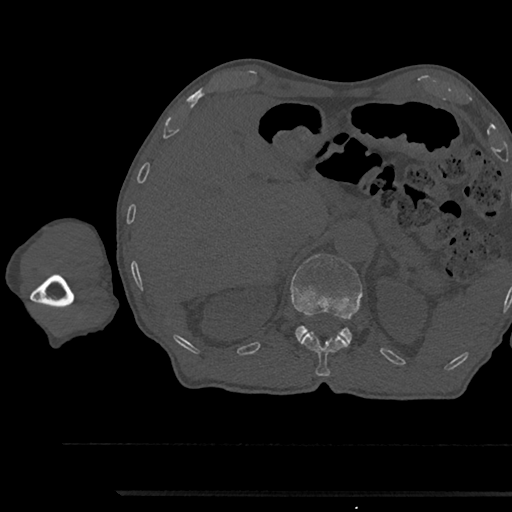
CT including the spine, one axial slice; slice 679 of 797 in the series (ordered by position); bone window (W 1800 / L 400 HU); 0.5 mm slice thickness; 512 × 512 image matrix, field of view 367 × 367 mm. Male patient, age 79 years. From the clinical record (not read from this slice): primary cancer: prostate.
Outlined on this slice (semi-automatically segmented with operator editing):
- L1 vertebra: bounding box <291,254,362,342> (left, top, right, bottom; pixels)
- T12 vertebra: <300,331,349,377>